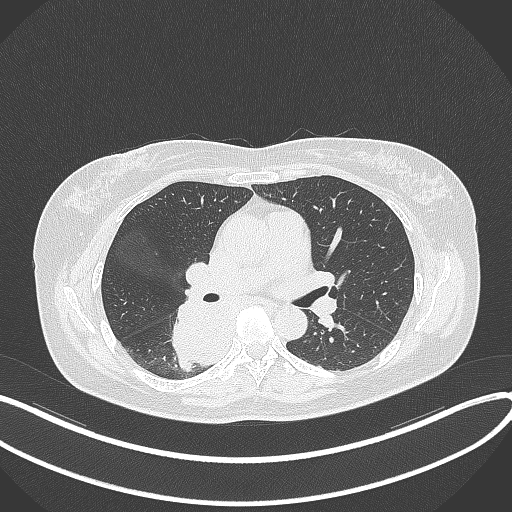
Chest CT, one axial slice; position 206 of 331 along the scan axis; reconstruction kernel B70f; 120 kVp; lung window (W 1500 / L -600 HU); 1 mm slice thickness; 512 × 512 image matrix, field of view 400 × 400 mm. Patient: female, 54 years. Case-level facts recorded for this patient, not image findings: clinical TNM (as recorded): T4 N0 M0.
Structures marked on this image (rectangle marked by the reading radiologist):
- lung tumour (recorded histology: adenocarcinoma): box from (x=171, y=303) to (x=232, y=371) px